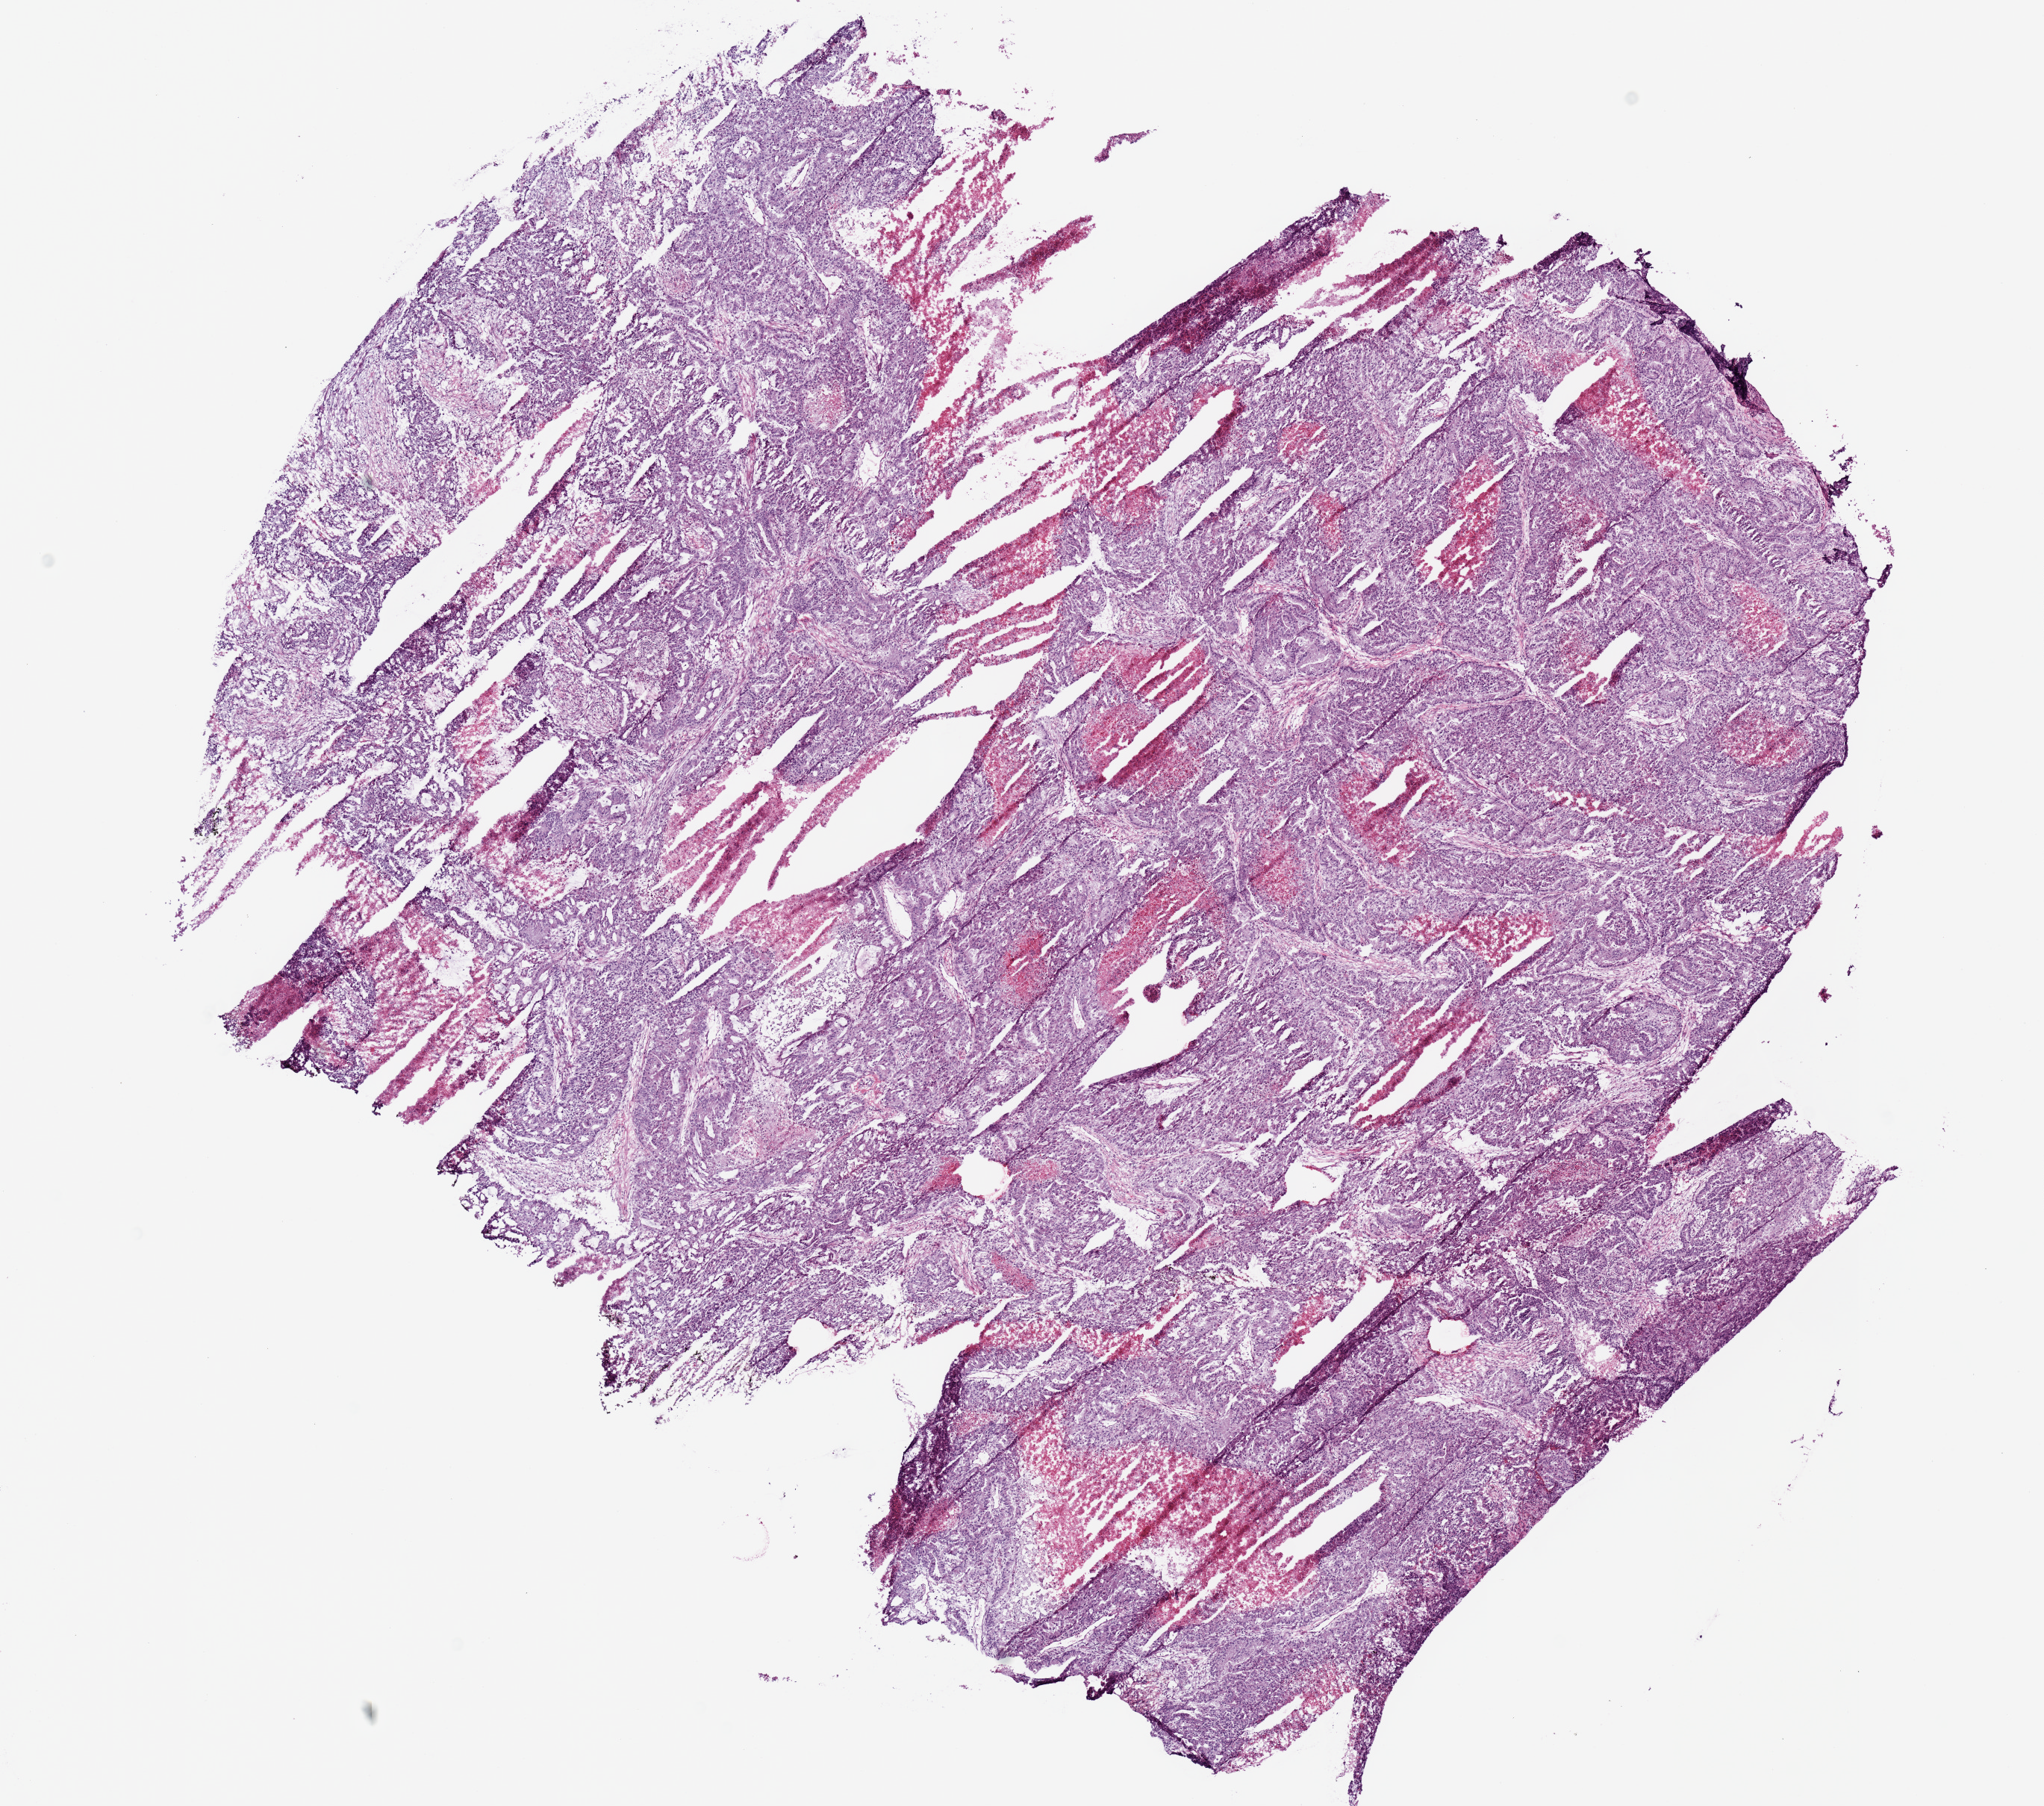
Digitized Hematoxylin and eosin (H&E) stained tissue section (whole slide) — low-resolution overview of the scanned area, about 10.8 x 9.6 mm; frozen section from the top of the tissue portion; sample: primary tumour, lung. Male, age 67 years at initial diagnosis. Pathologist review of this section (percent, as recorded): tumour nuclei 75%, necrosis 20%.
Histologic diagnosis: Adenocarcinoma, NOS (middle lobe, lung). TNM: T3 N2 MX. AJCC pathologic stage: IIIA (7th edition).